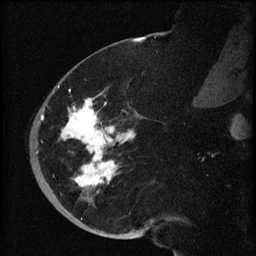
Breast MRI (dynamic contrast-enhanced), one sagittal slice. Slice 23 of 60 in the series (ordered by position). Dynamic contrast-enhanced series, image 2 of 3 at this slice position (ordered by acquisition). 1.5 T. TE 4.2 ms, TR 8.2 ms. 2 mm slice thickness. 256 × 256 image matrix. Patient: female, 71 years.
Annotated regions visible in this slice (semi-automatic segmentation, software-assisted and operator-edited):
- analysis volume of interest (the breast-tissue region the enhancement analysis was run in; not a lesion): box from (x=40, y=72) to (x=147, y=196) px
- tumour enhancement mask (voxels above the 70 % enhancement threshold inside the analysis volume of interest): (x=41, y=86)–(x=135, y=187)